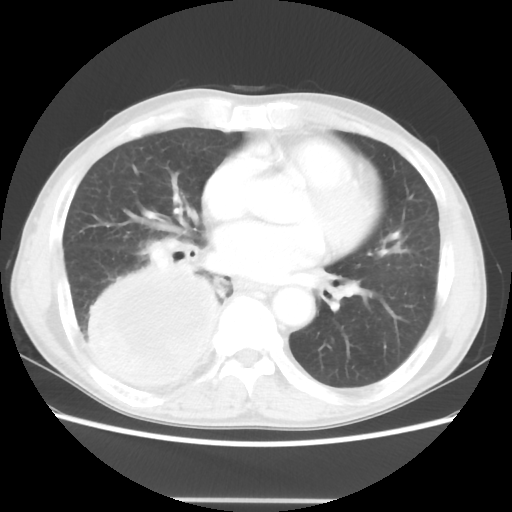
Chest CT, one axial slice. Position 19 of 48 along the scan axis. Reconstruction kernel STANDARD. 100 kVp. Lung window (W 1500 / L -600 HU). 512 × 512 image matrix, field of view 361 × 361 mm. Patient: male, 66 years. Case-level facts recorded for this patient, not image findings: clinical TNM (as recorded): T4 N1 M1; histopathological grade: G3.
Annotated regions visible in this slice (rectangle marked by the reading radiologist):
- lung tumour (recorded histology: small cell carcinoma): bounding box <70,256,230,394> (left, top, right, bottom; pixels)